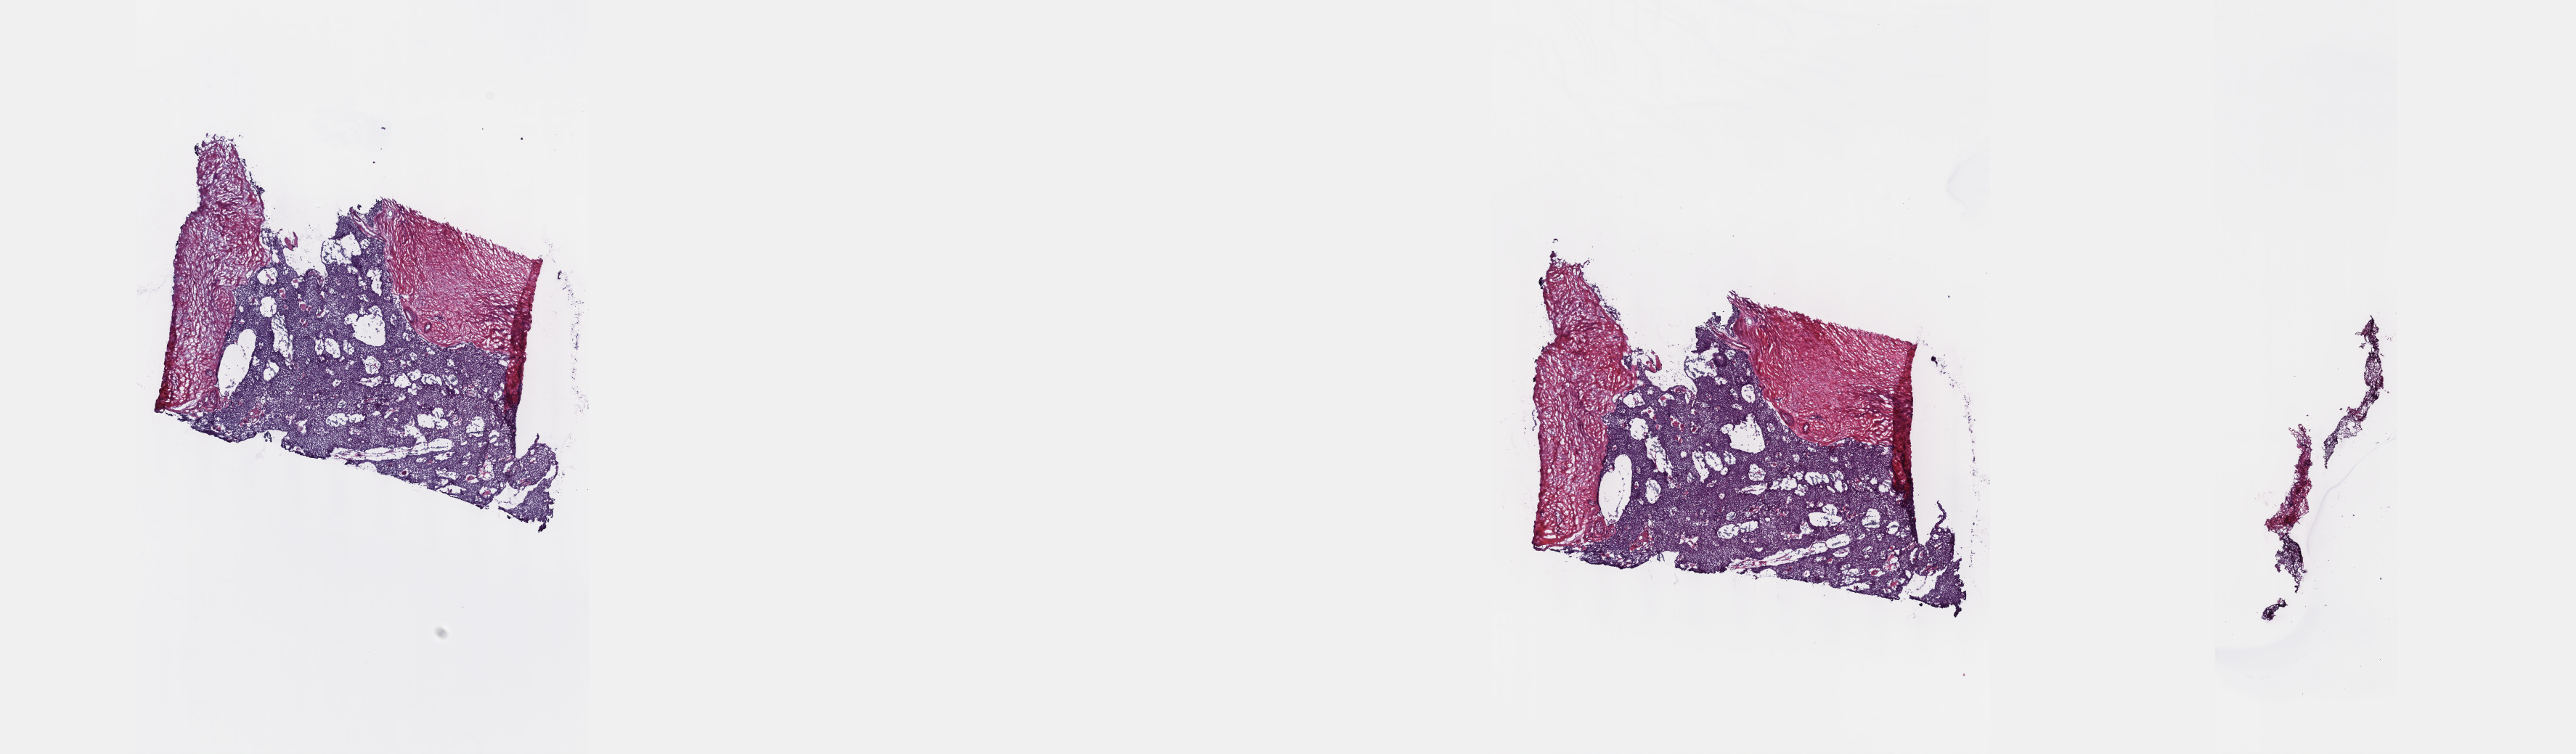
Whole-slide histology image, H&E — whole scanned area (about 28.7 x 8.4 mm, acquisition: 40x scan) shown as a low-resolution overview. Frozen section. Sample: primary tumour, thymus. Female, age 61 years at initial diagnosis. Slide review estimates, as recorded: tumour cells 75%, tumour nuclei 75%, normal cells 0%, stromal cells 25%, necrosis 0%. Inflammatory infiltration, as recorded: lymphocyte infiltration 2%, monocyte infiltration 0%, neutrophil infiltration 0%.
Histologic diagnosis: Thymoma, type B3, malignant.